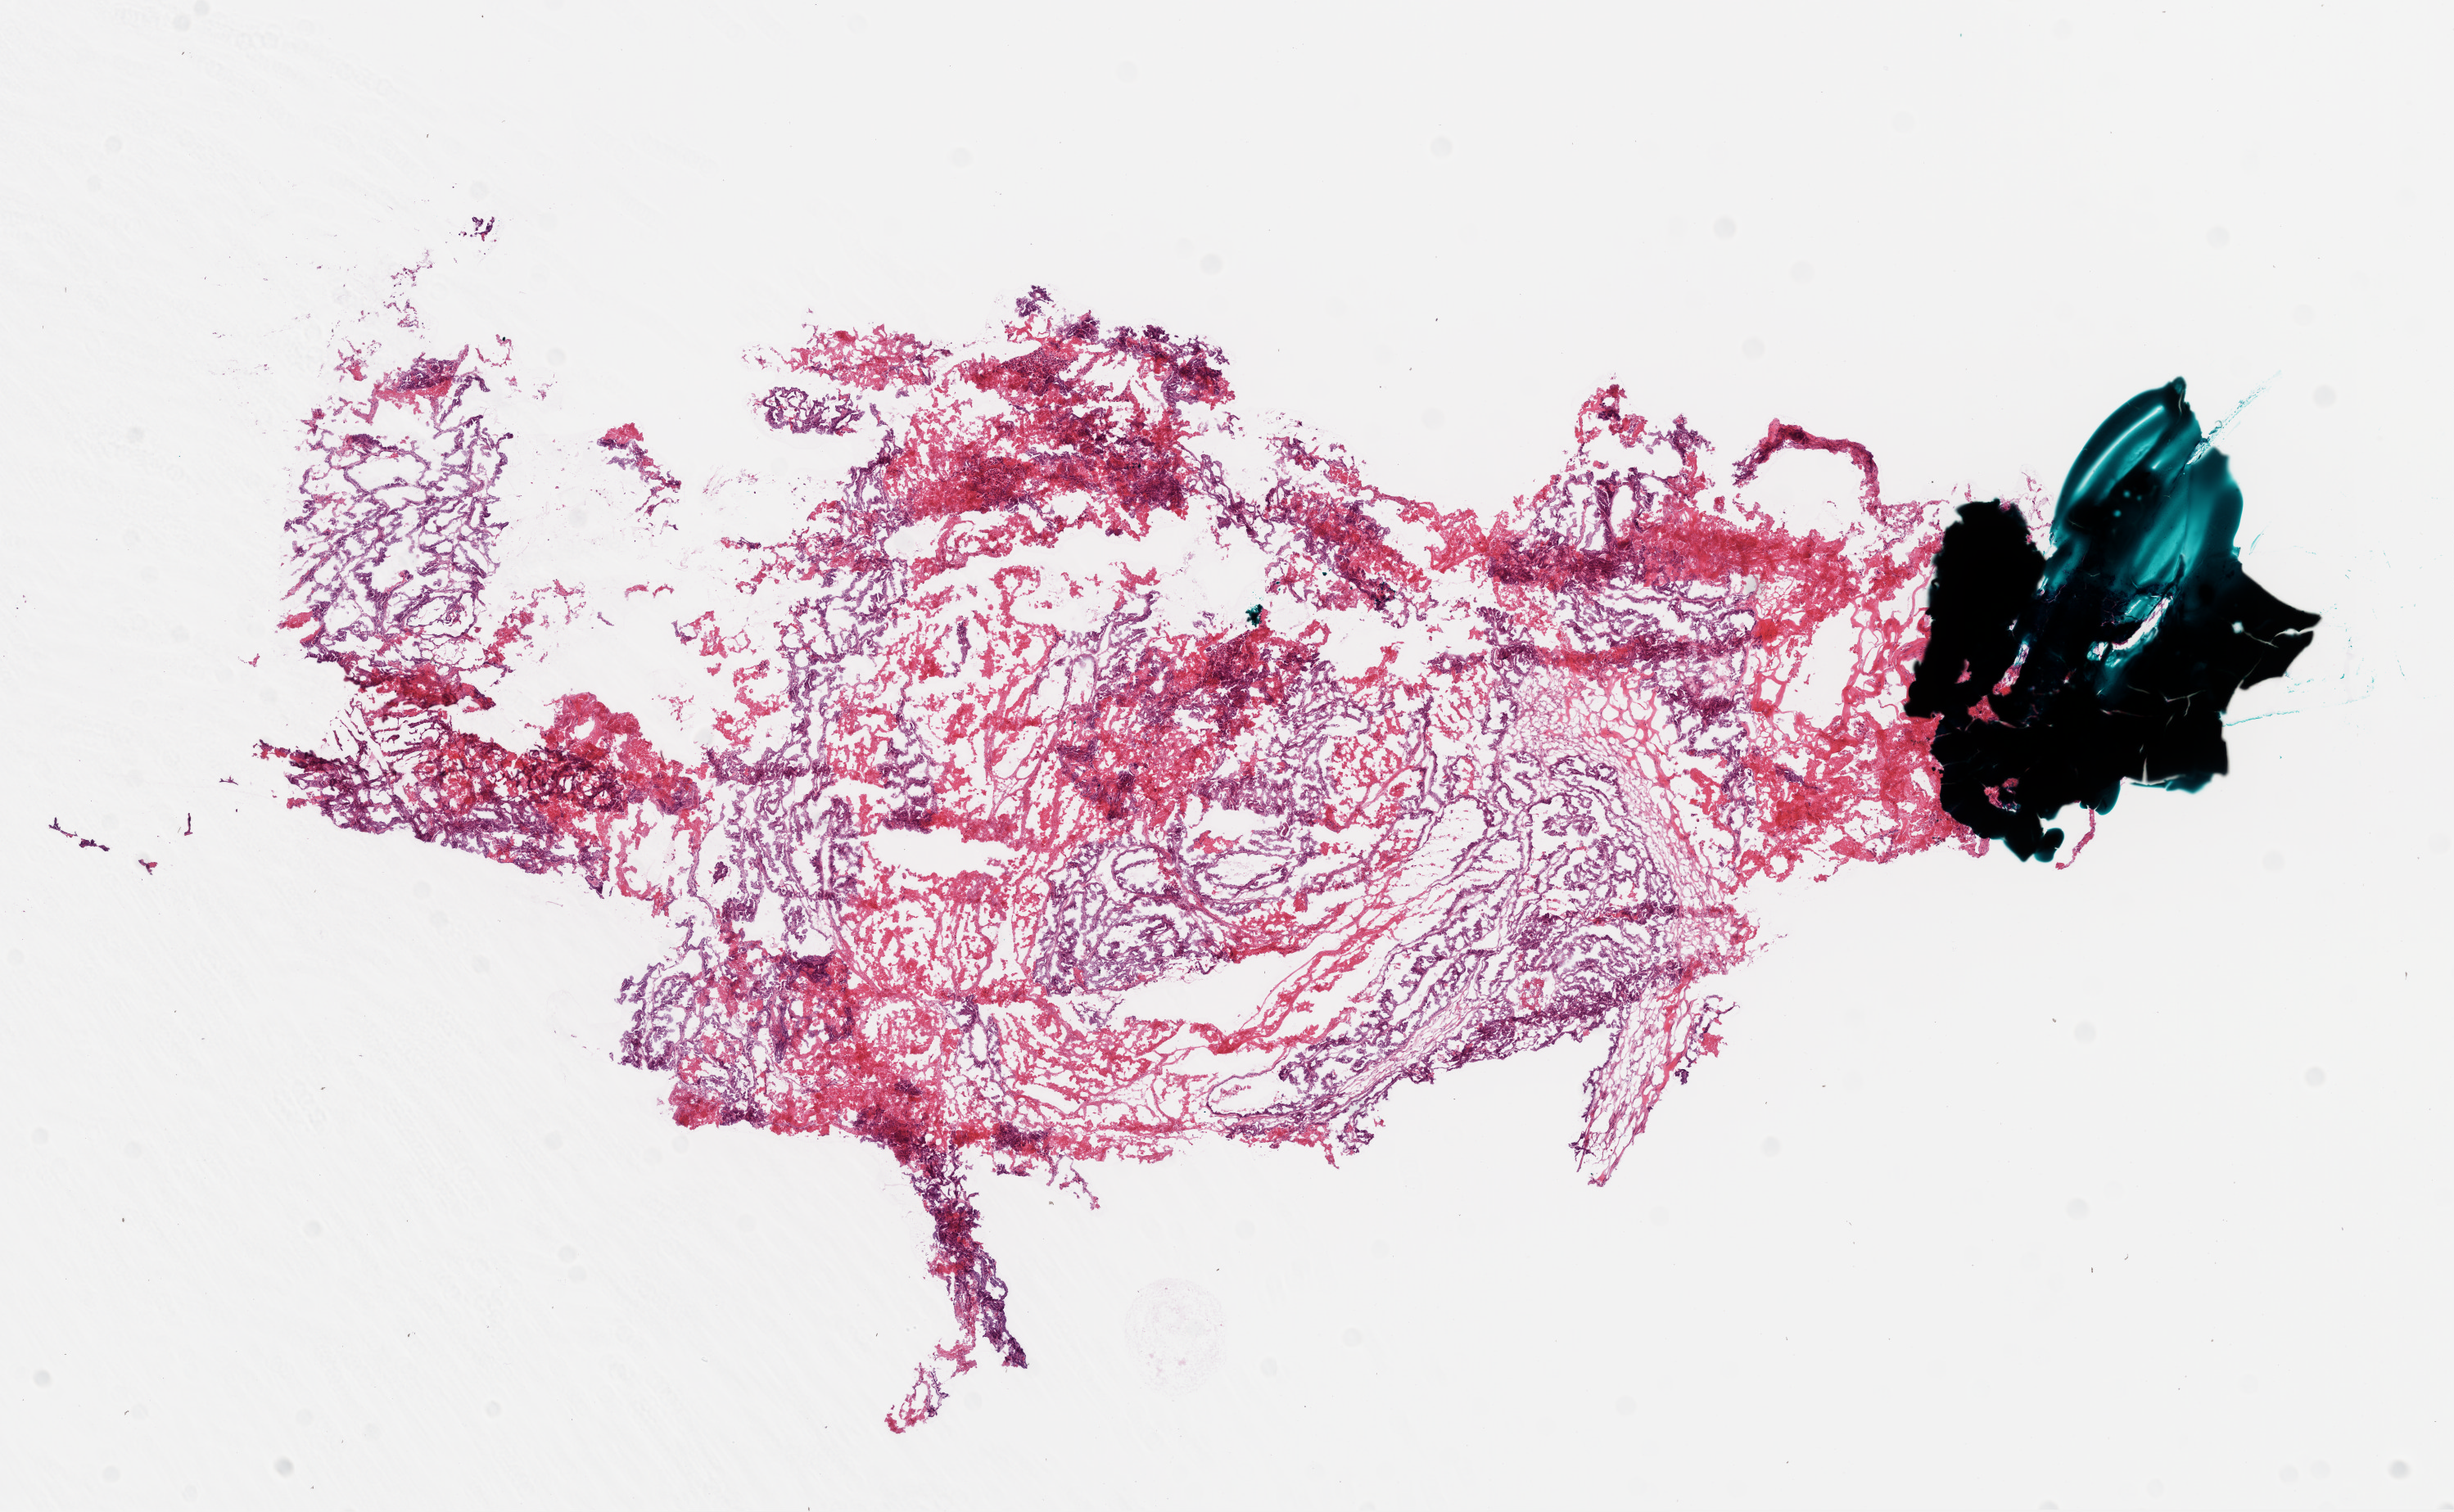
H&E-stained whole-slide image — a low-resolution overview of the entire scanned area, about 12.1 x 7.4 mm (slide scanned at 20x). Frozen section. Ovary, primary tumour sample. Female patient; age at initial diagnosis 73 years. Pathologist review of this section (percent, as recorded): tumour cells 75%, tumour nuclei 85%.
Histologic diagnosis: Serous cystadenocarcinoma, NOS.